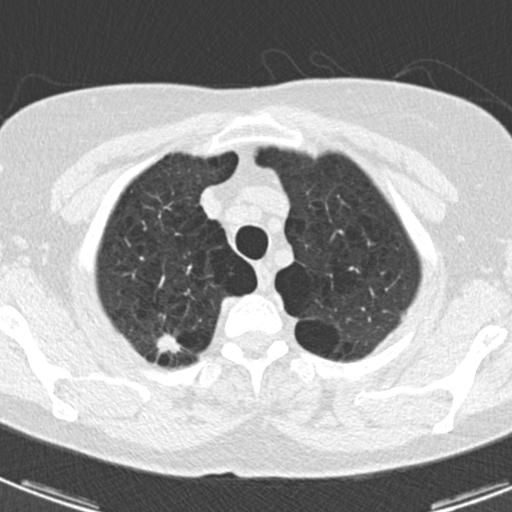
Low-dose screening chest CT, one axial slice. Slice 153 of 174 in the series (ordered by position). Lung window (W 1500 / L -600 HU). 2 mm slice thickness. 512 × 512 image matrix, field of view 281 × 281 mm.
Structures marked on this image (outlined manually by an expert reader):
- lesion 1 (tumor, upper lobe of right lung): bounding box <157,334,180,353> (left, top, right, bottom; pixels)